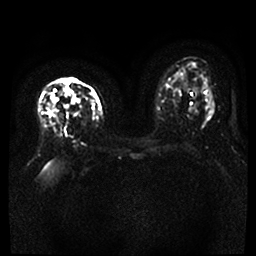
Breast MRI, one axial slice. Position 18 of 46 along the scan axis. Diffusion-weighted series; image 2 of 4 stored at this slice position (different b-values; order by instance number). 1.5 T. 4 mm slice thickness. 256 × 256 image matrix, field of view 360 × 360 mm. Female patient.
Annotated regions visible in this slice (outlined manually by an expert reader):
- tumour on diffusion-weighted imaging: bounding box (x1, y1, x2, y2) in pixels: (52, 89, 79, 103)